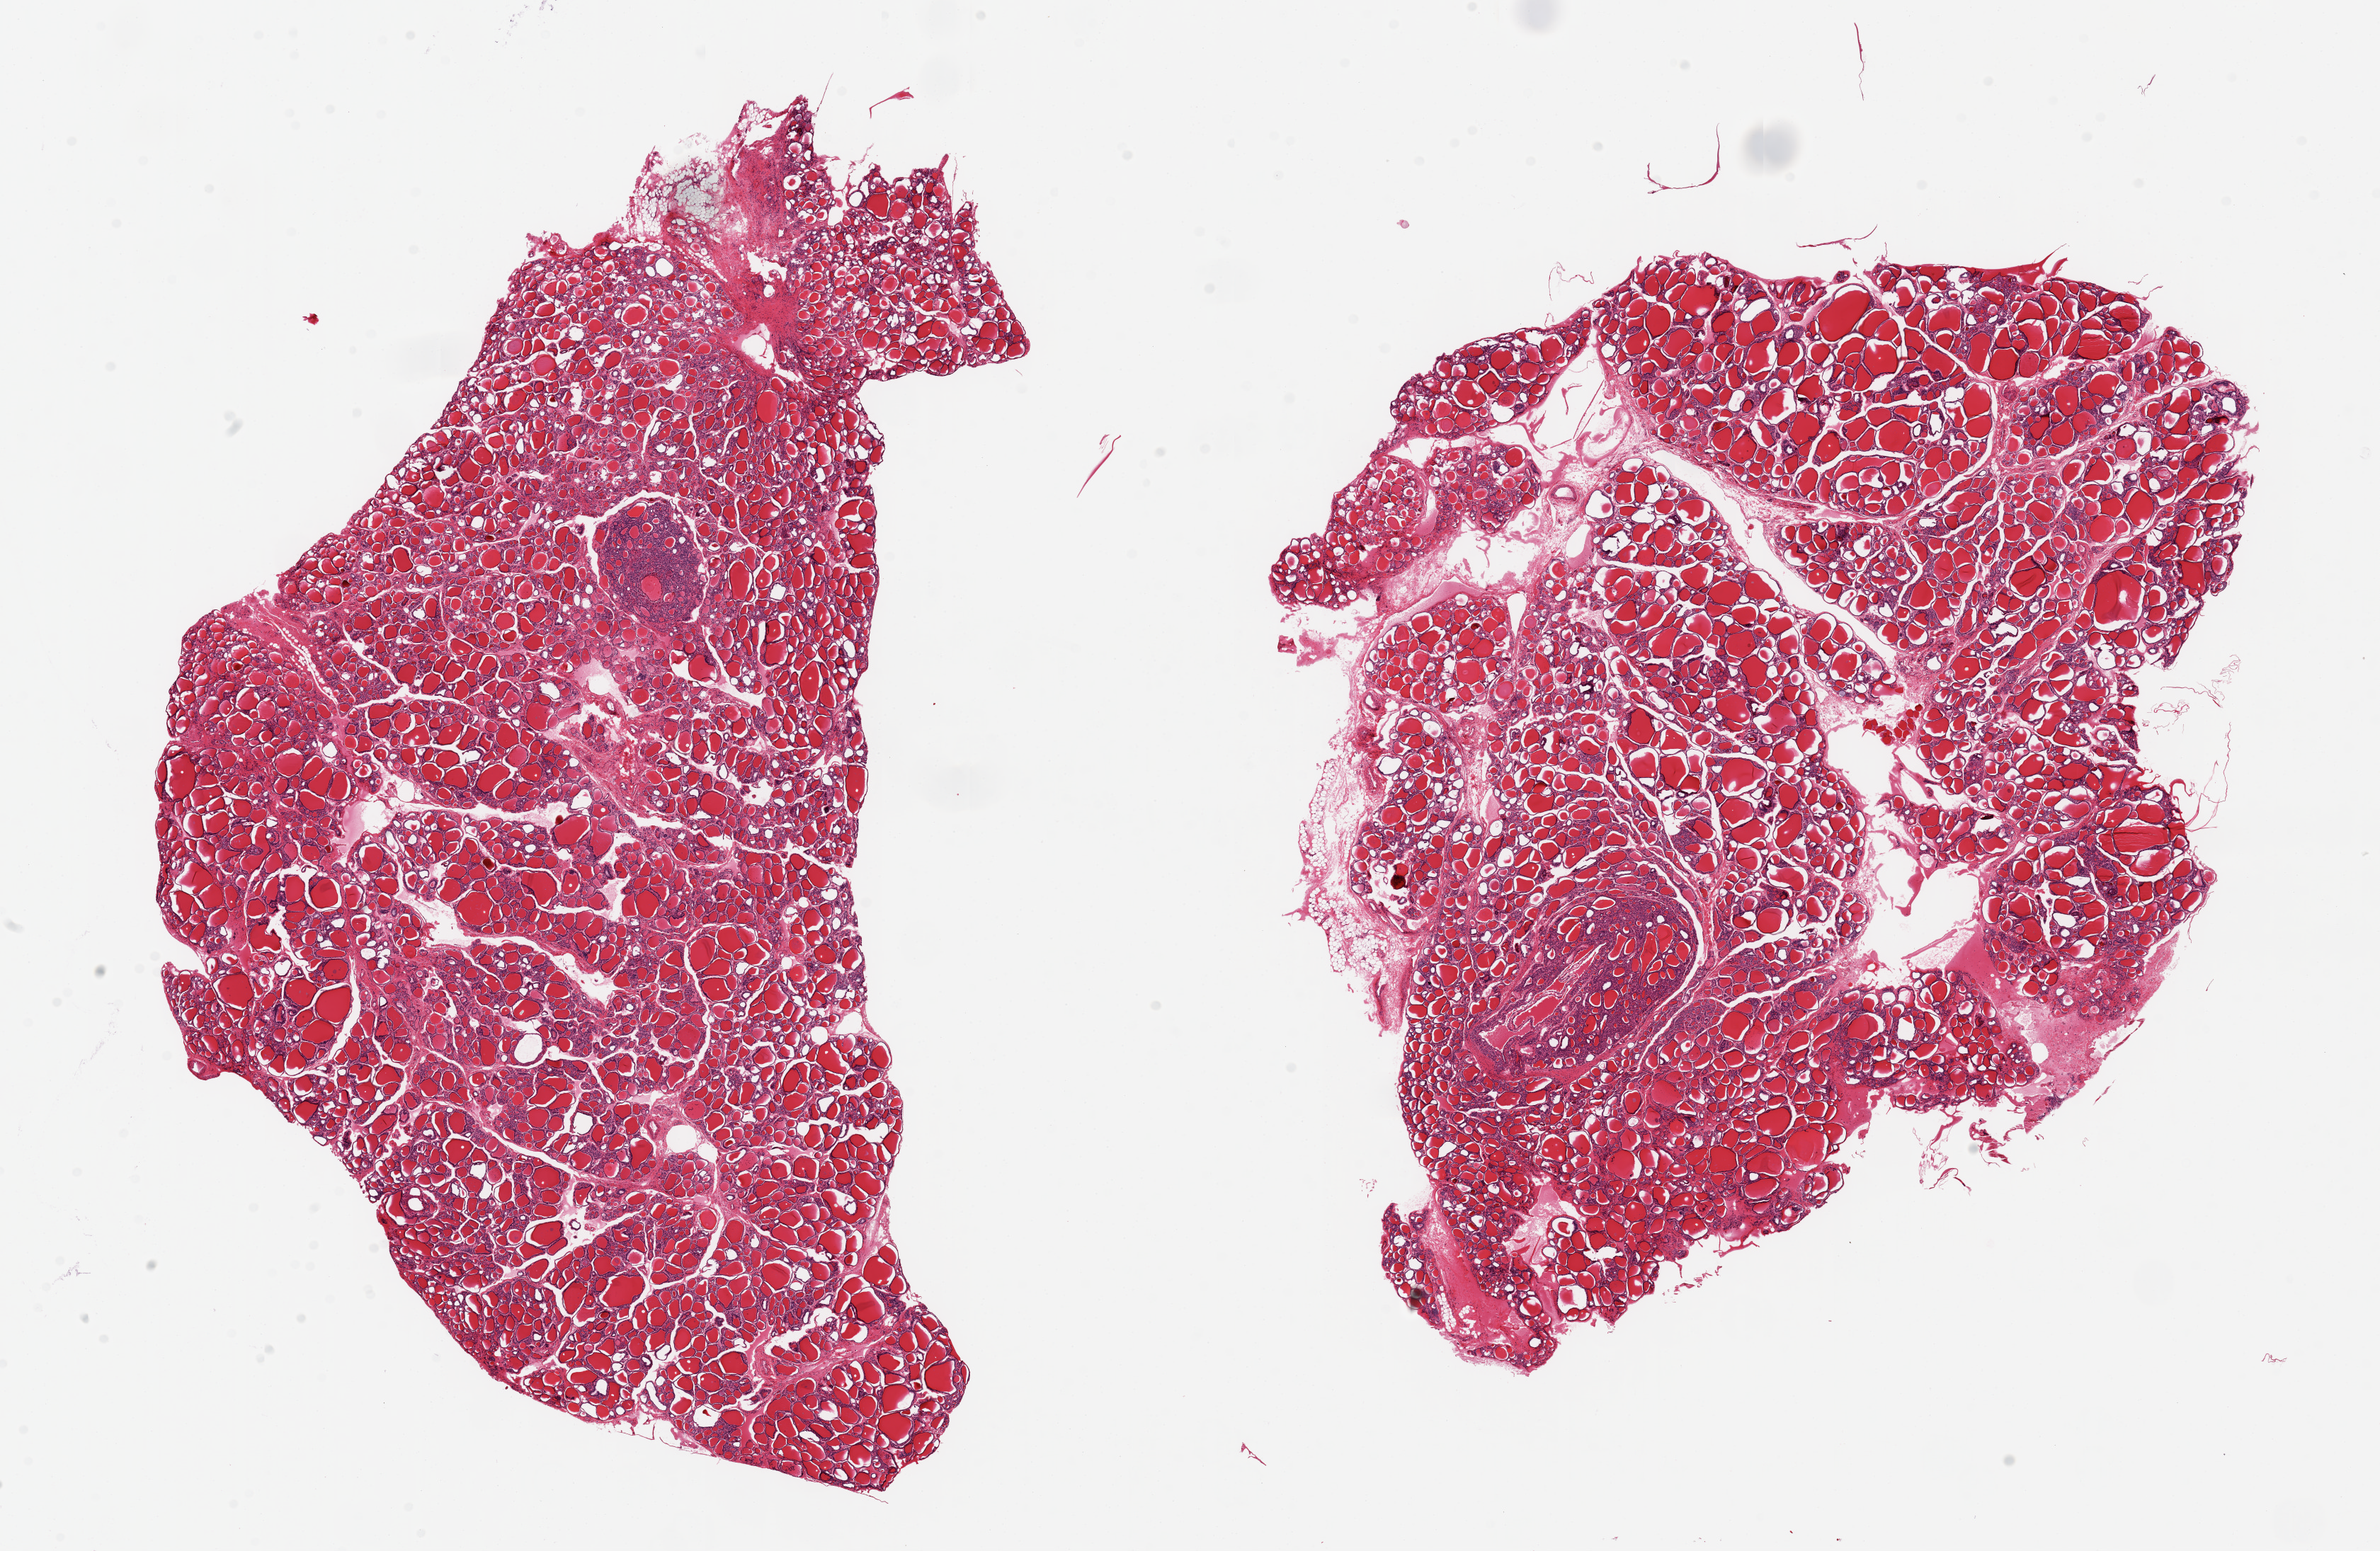
Whole-slide image, H&E stain, brightfield — whole scanned area (about 26.6 x 17.3 mm) shown as a low-resolution overview. PAXgene-fixed, paraffin-embedded tissue. Target tissue: thyroid. Tissue donor sample.
Pathologist's review note for this sample: 2 pieces, 16x10 & 12x11mm.